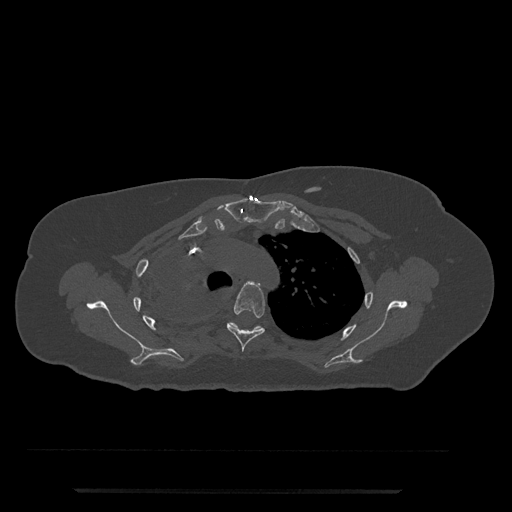
CT including the spine, one axial slice. 120 kVp. Bone window (W 1800 / L 400 HU). 0.5 mm slice thickness. 512 × 512 image matrix. Patient: female, 51 years. From the clinical record (not read from this slice): primary cancer: neuro; vertebrae with lytic lesions (as recorded): T8.
Annotated regions visible in this slice (semi-automatically segmented with operator editing):
- T4 vertebra: box from (x=227, y=282) to (x=265, y=352) px
- T5 vertebra: (x=228, y=322)–(x=263, y=331)